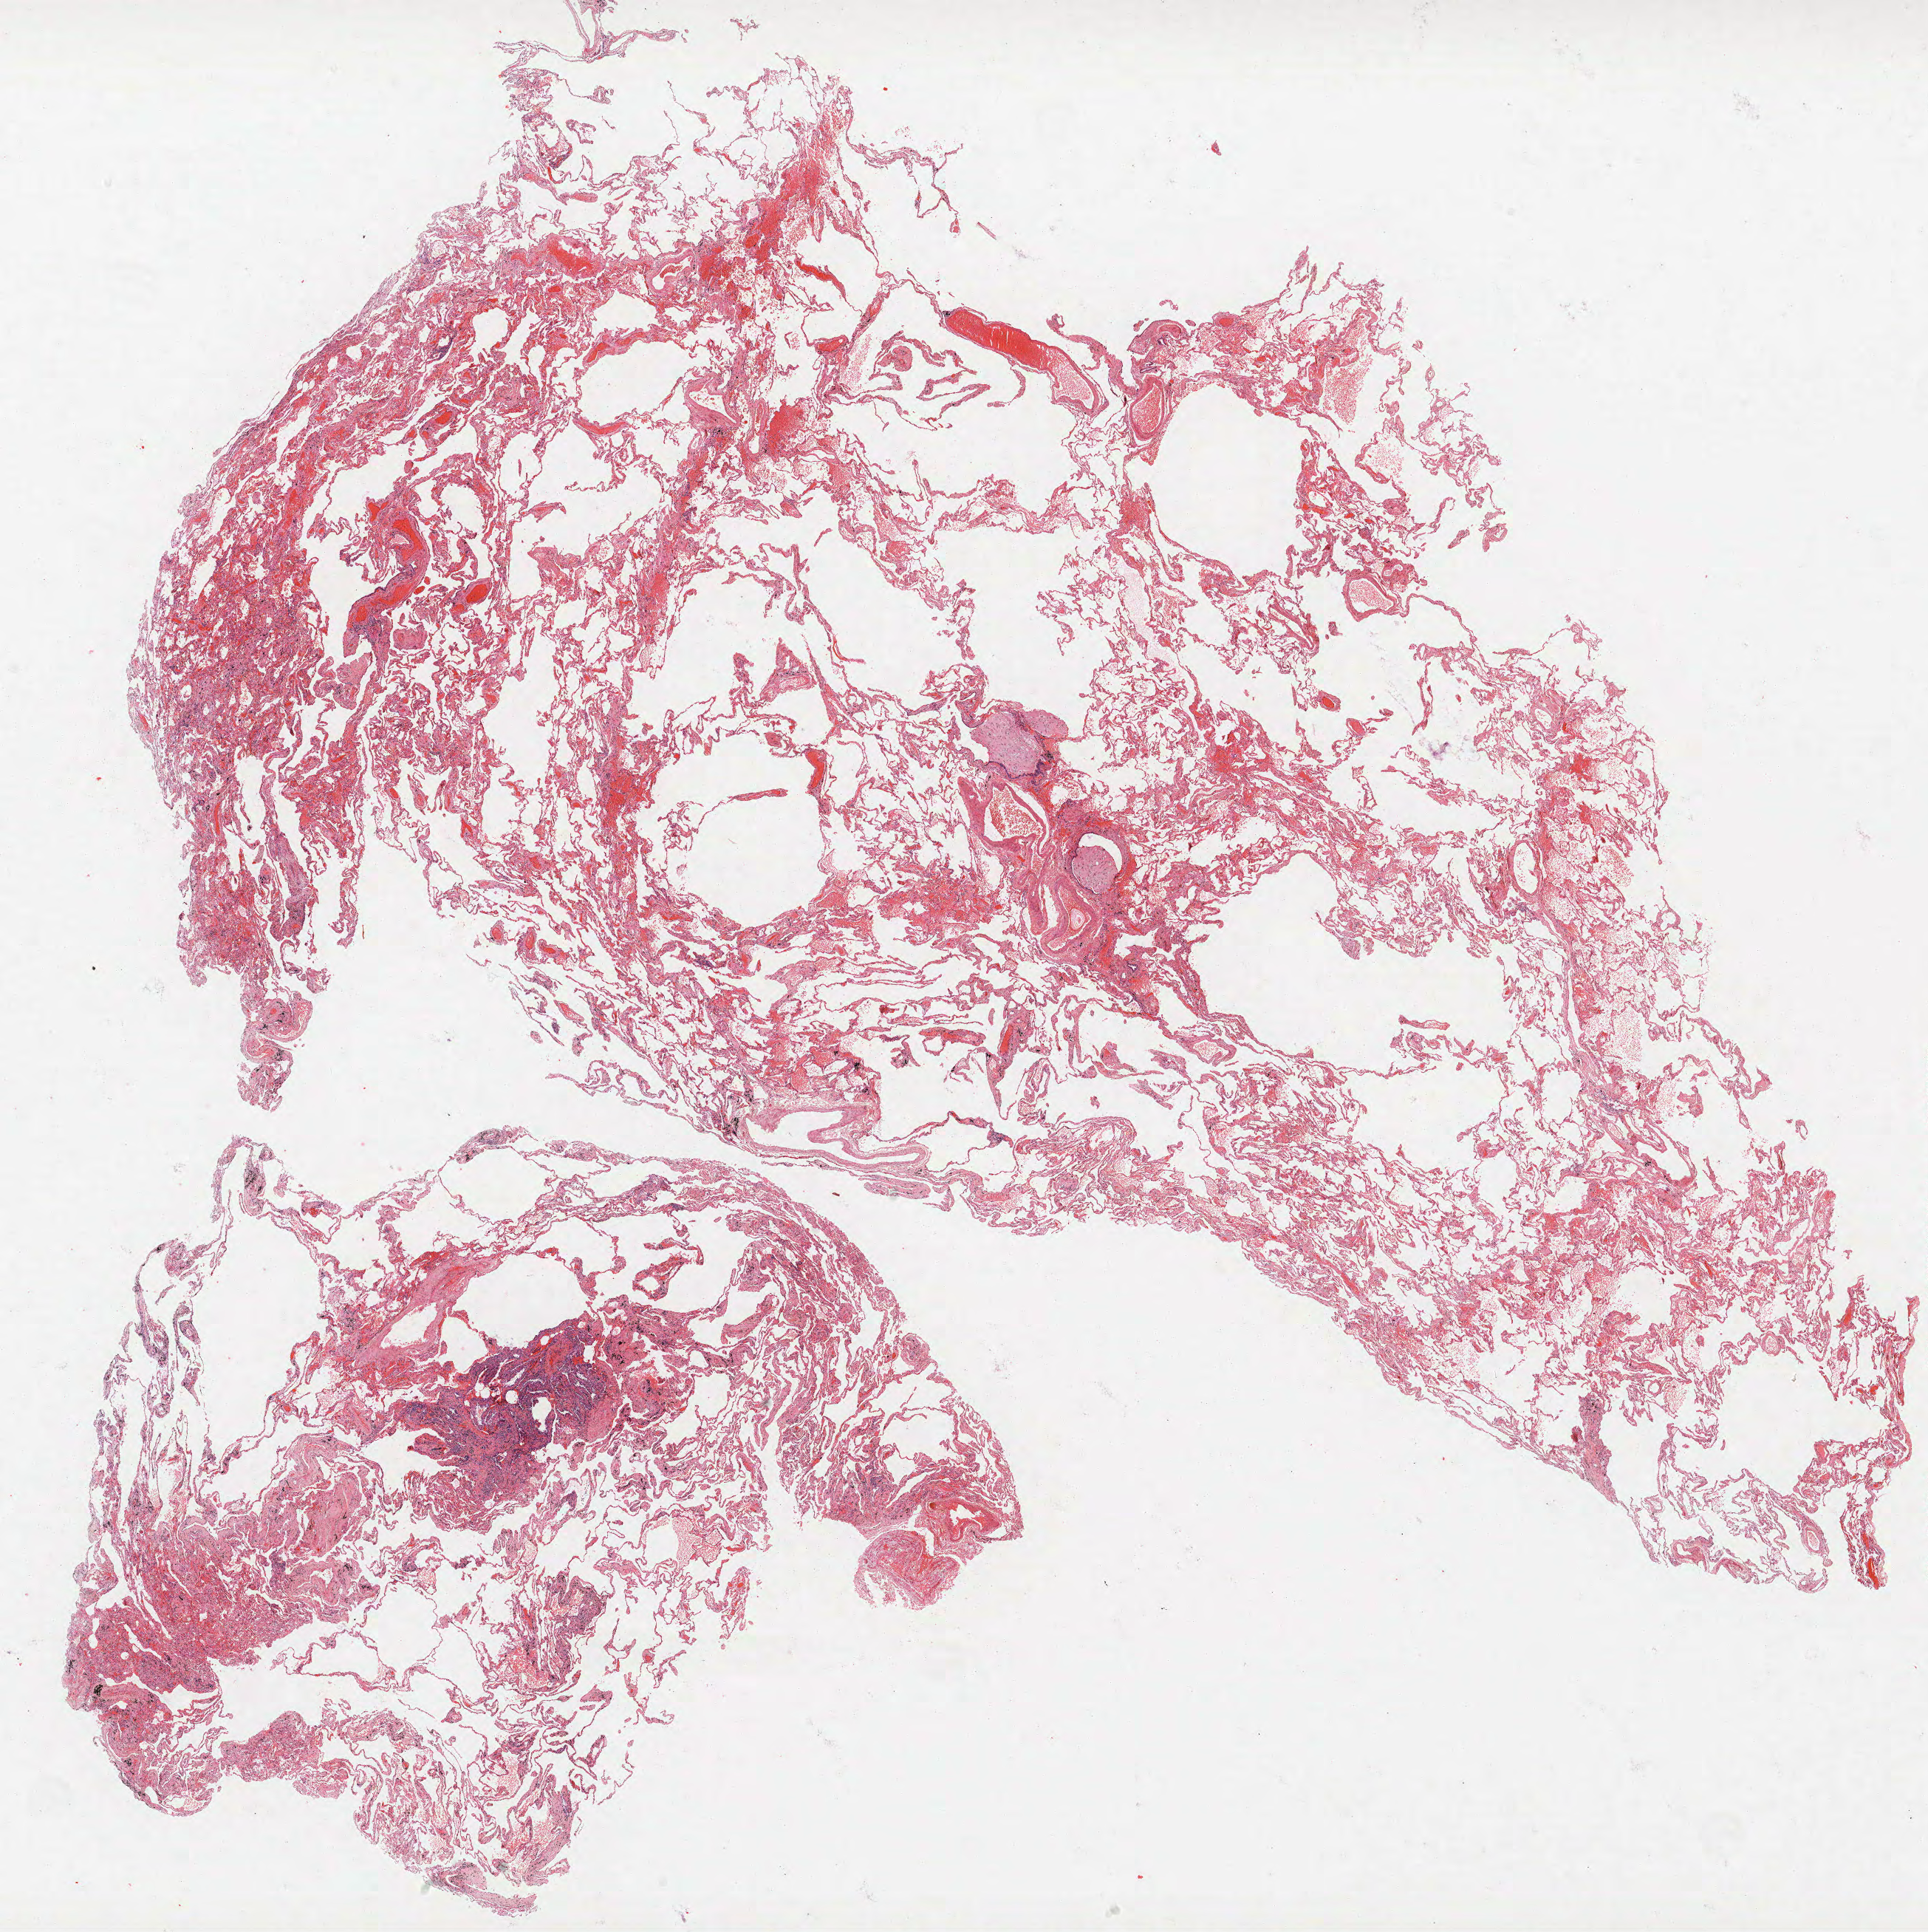
H&E whole-slide image, whole scanned area (about 20.9 x 20.9 mm) shown as a low-resolution overview; formalin-fixed paraffin-embedded (FFPE) section; lung. Male patient, aged 74 at enrolment. Former smoker at enrolment. Grade: poorly differentiated (G3).
Tumour size (pathology): 6 mm. Primary tumour location (clinical record): right upper lobe. Stage (AJCC 6th edition): IA. Participant's lung-cancer diagnosis: Adenocarcinoma, NOS (ICD-O-3 8140/3).